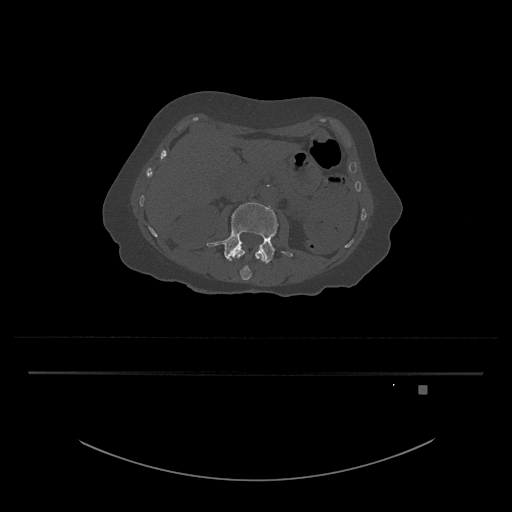
CT including the spine, one axial slice. Slice 450 of 797 in the series (ordered by position). Reconstruction kernel Br40s/3. 120 kVp. Bone window (W 1800 / L 400 HU). 0.5 mm slice thickness. 512 × 512 image matrix, field of view 500 × 500 mm. Female patient, age 57 years. Case-level facts recorded for this patient, not image findings: primary cancer: cervical.
Outlined on this slice (semi-automatic segmentation, software-assisted and operator-edited):
- L3 vertebra: bounding box [x1, y1, x2, y2] px = [207, 202, 292, 264]